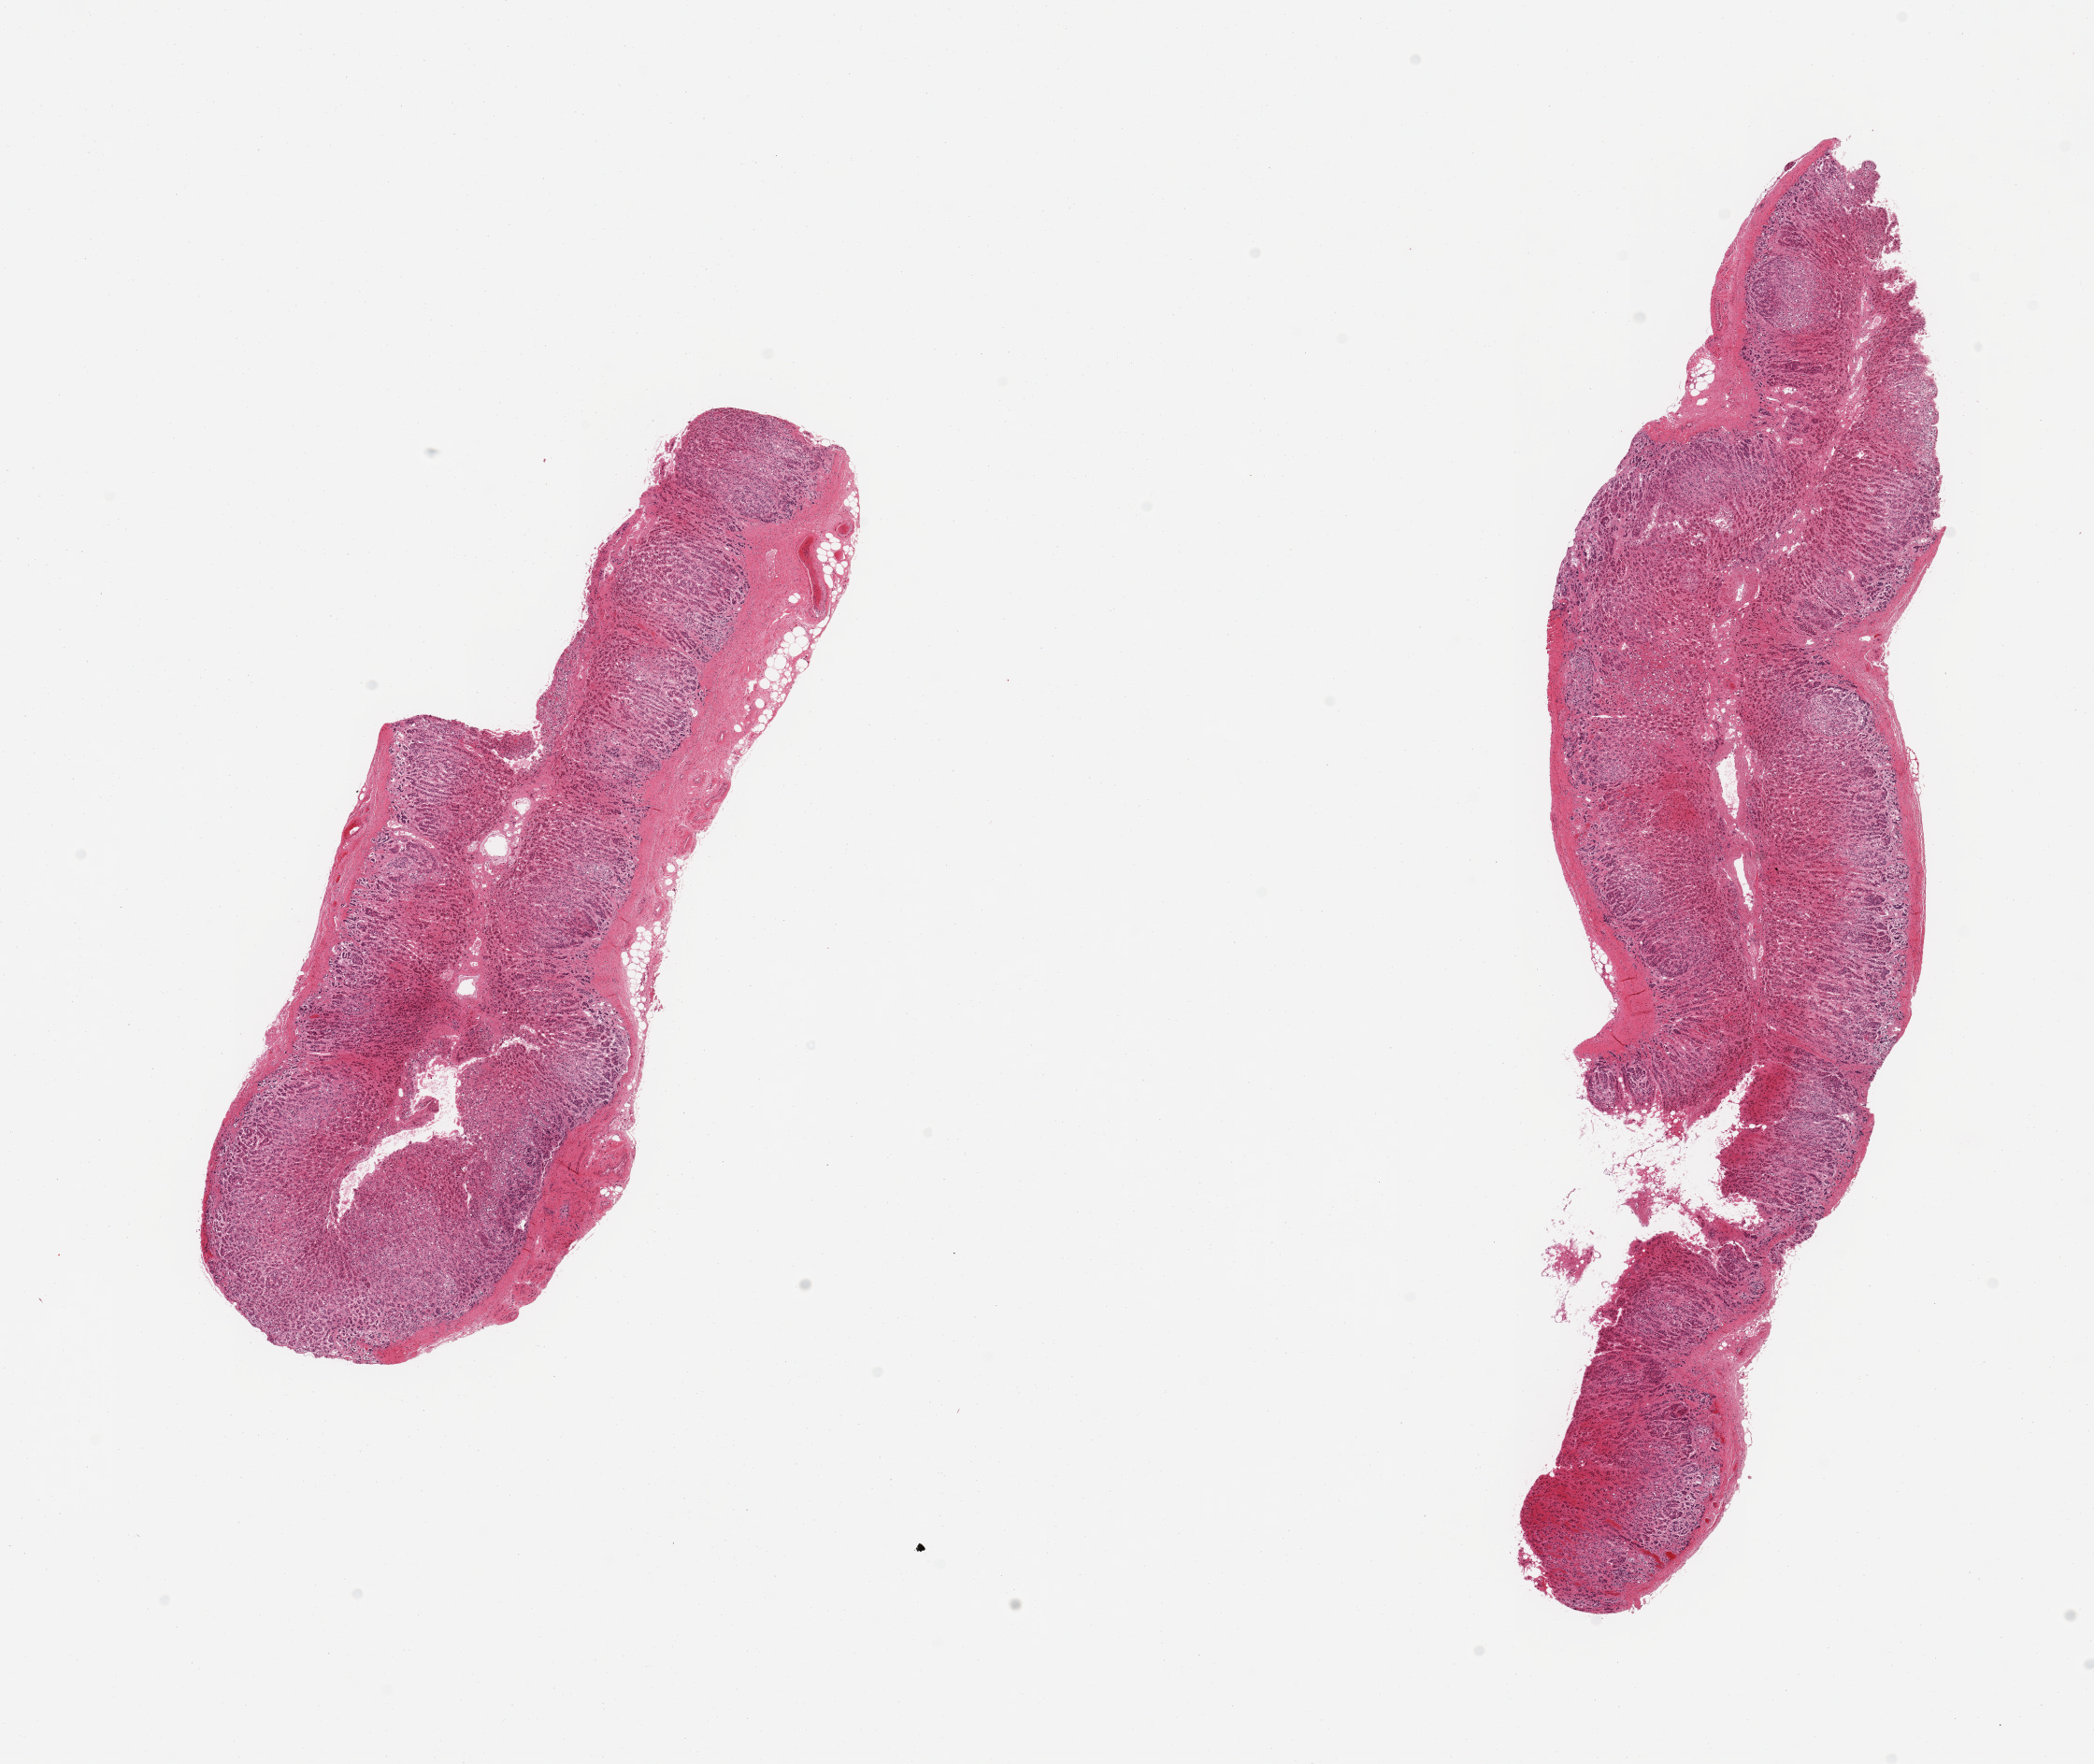
Digitized H&E-stained section, brightfield — a low-resolution overview of the entire scanned area, about 17.7 x 14.9 mm, PAXgene-fixed, paraffin-embedded tissue, sampled site (target tissue): adrenal gland, tissue donor sample. Donor sex: female.
Reviewer comment on this tissue sample: 2 pieces; well dissected but poorly preserved.